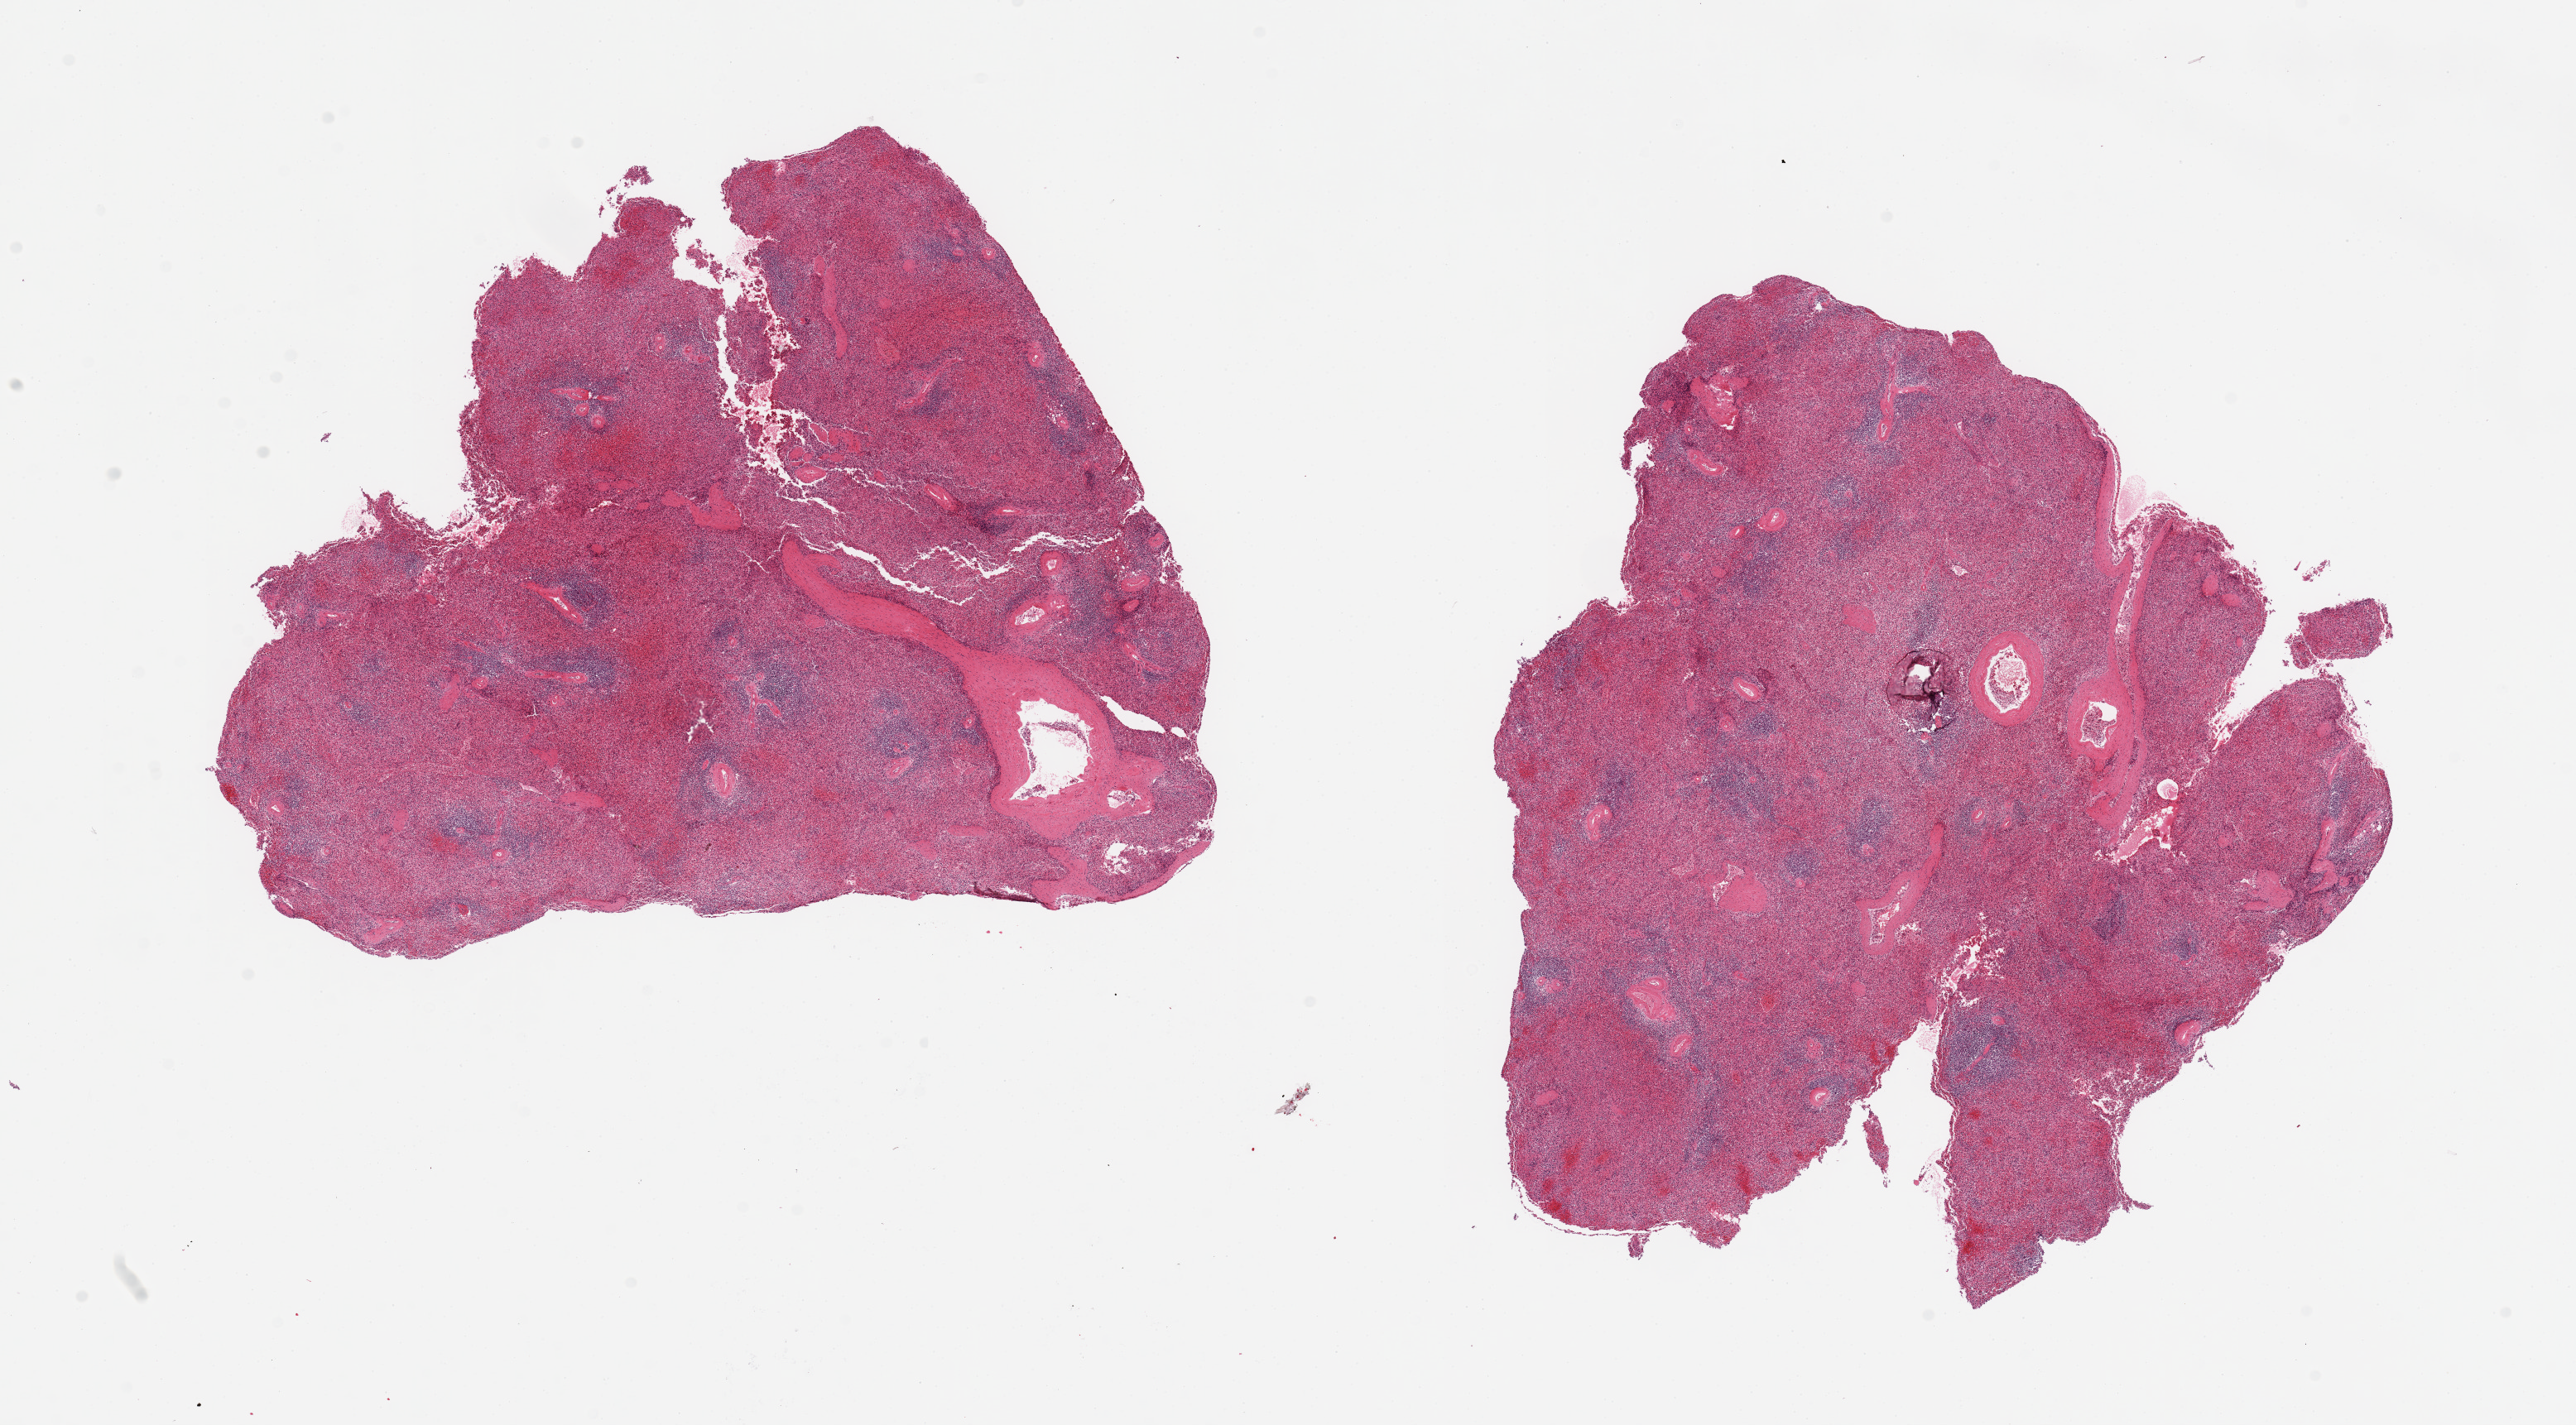
Digitized H&E-stained section, brightfield, shown as a low-resolution overview of the whole scanned area (about 24.6 x 13.6 mm). PAXgene-fixed, paraffin-embedded tissue. Sampled site (target tissue): spleen. Tissue donor sample.
• review note (as recorded): 2 pieces